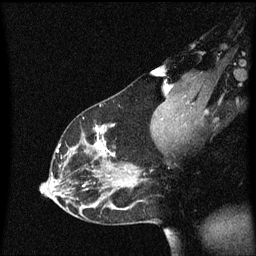
Breast MRI (dynamic contrast-enhanced), one sagittal slice; slice 36 of 60 in the series (ordered by position); dynamic contrast-enhanced series, image 2 of 3 at this slice position (ordered by acquisition); 1.5 T; TE 4.2 ms, TR 8.4 ms; 2 mm slice thickness; 256 × 256 image matrix, field of view 200 × 200 mm. Patient: female, 33 years.
Structures marked on this image (semi-automatically segmented with operator editing):
- analysis volume of interest (the breast-tissue region the enhancement analysis was run in; not a lesion): bounding box [x1, y1, x2, y2] px = [45, 114, 152, 191]
- tumour enhancement mask (voxels above the 70 % enhancement threshold inside the analysis volume of interest): [56, 126, 131, 187]